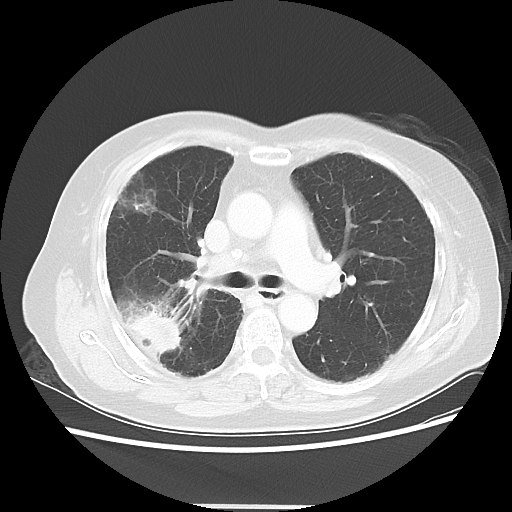
Chest CT, one axial slice; reconstruction kernel LUNG; 120 kVp; lung window (W 1500 / L -600 HU); 5 mm slice thickness; 512 × 512 image matrix, field of view 360 × 360 mm. Patient: female, 72 years. From the clinical record (not read from this slice): clinical TNM (as recorded): T2 N1 M0; histopathological grade: G1.
Annotated regions visible in this slice (rectangle marked by the reading radiologist):
- lung tumour (recorded histology: adenocarcinoma): bounding box <122,305,181,355> (left, top, right, bottom; pixels)